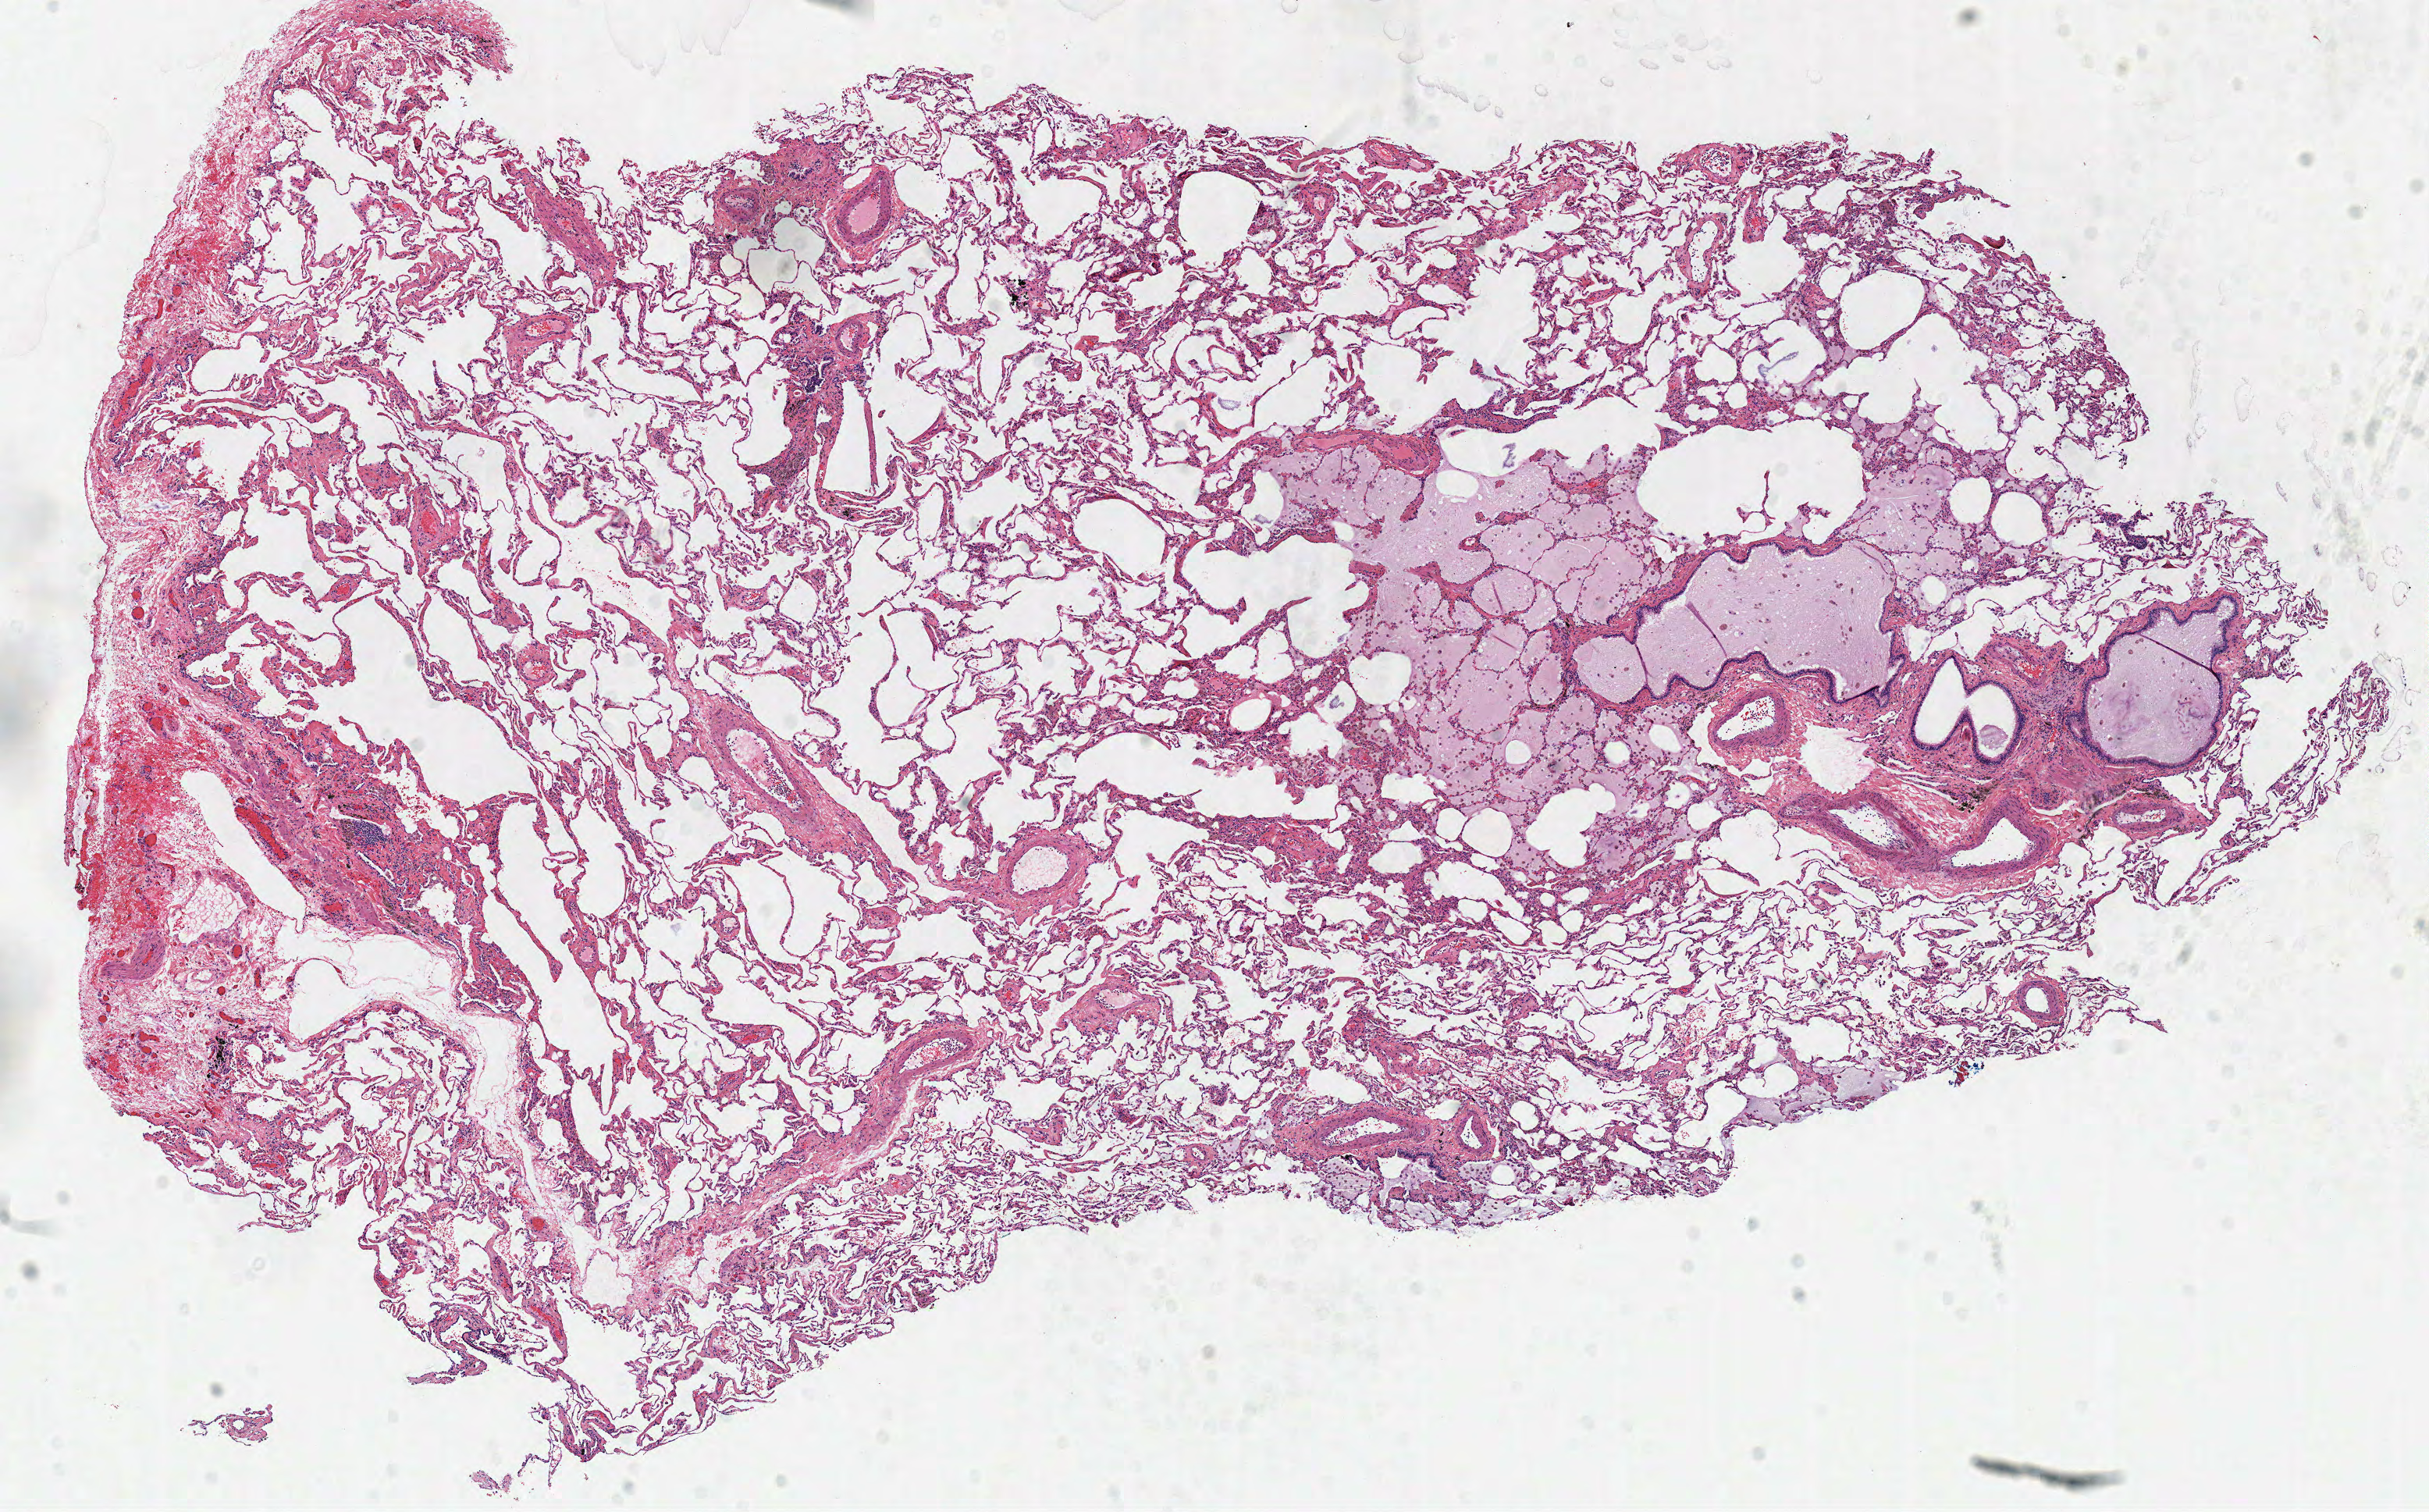
Whole-slide histology image, H&E, a low-resolution overview of the entire scanned area, about 12.2 x 7.6 mm (from a 40x scan). Frozen section from the top of the tissue portion. Sample: solid tissue normal (non-tumour tissue), lung. Female, age 50 years at initial diagnosis.
This section: solid tissue normal sample (biorepository sample class). Patient diagnosis: Adenocarcinoma, NOS.